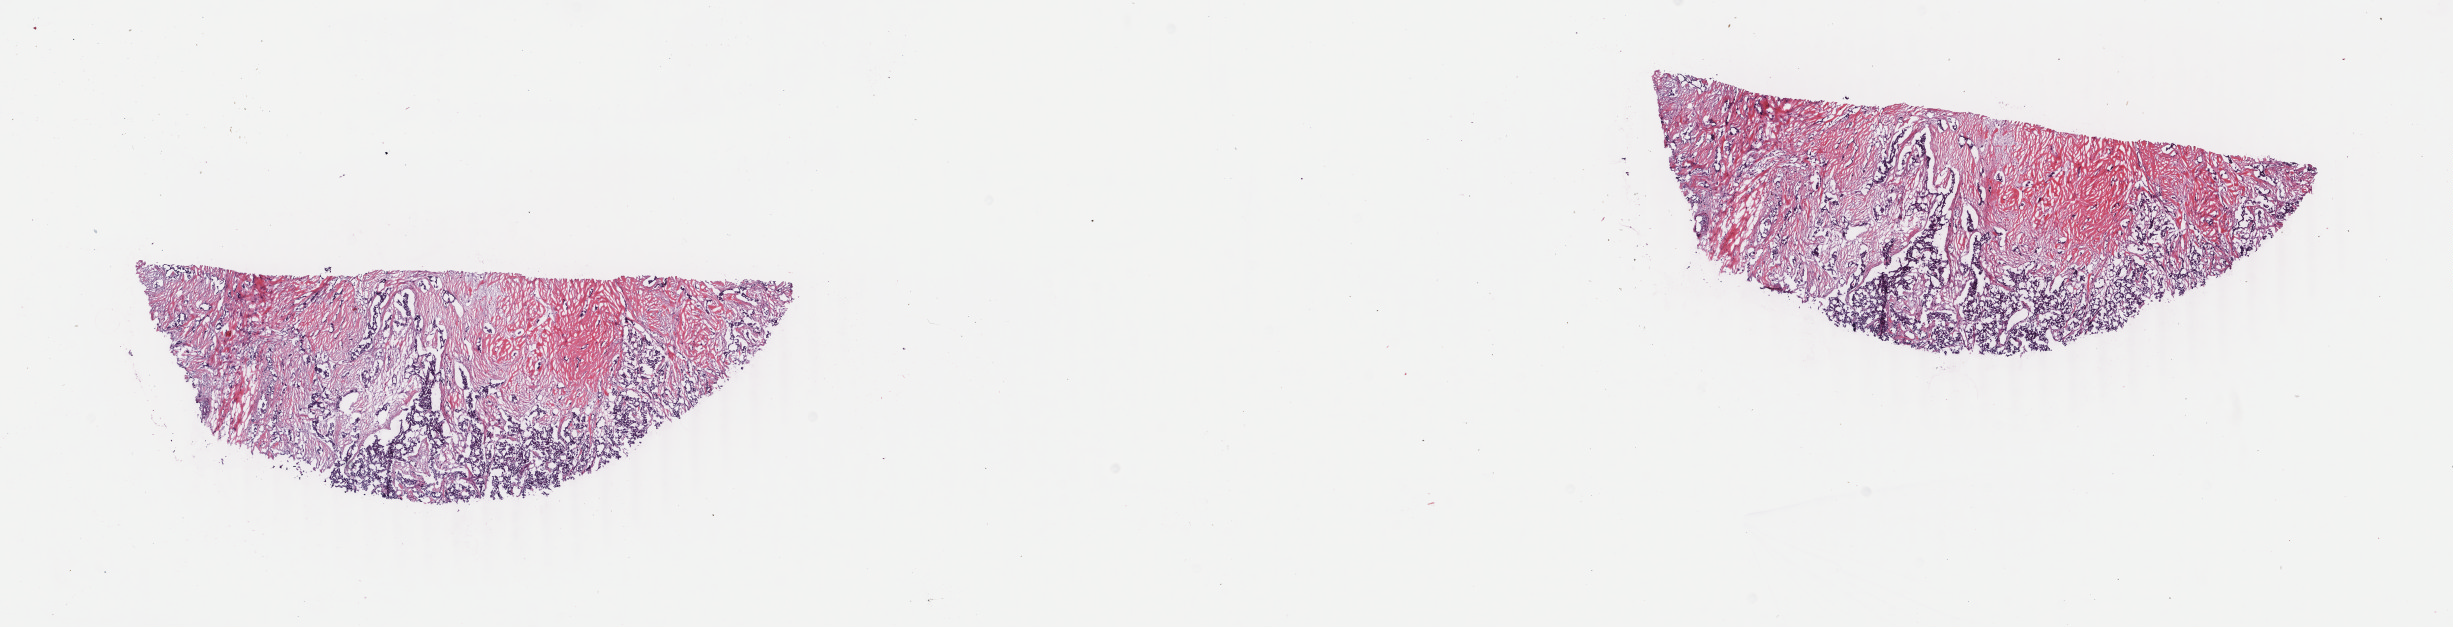
Whole-slide histology image, Hematoxylin and eosin (H&E) stained, low-resolution overview of the scanned area, about 19.5 x 5.0 mm (slide scanned at 40x), frozen section from the bottom of the tissue portion, breast, primary tumour sample. Female, age 51 years at initial diagnosis. Slide review estimates, as recorded: tumour cells 40%, tumour nuclei 60%, normal cells 0%, stromal cells 60%, necrosis 0%. Infiltration values recorded for this section: lymphocyte infiltration 0%, monocyte infiltration 0%, neutrophil infiltration 0%.
• diagnosis: Infiltrating duct carcinoma, NOS
• laterality: left
• AJCC pathologic stage: IIA (6th edition)